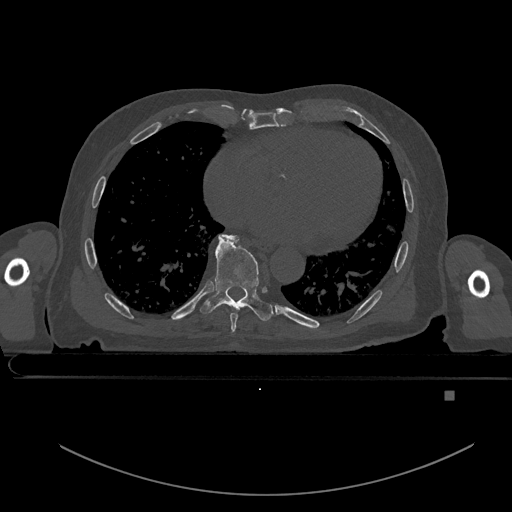
CT including the spine, one axial slice. Position 214 of 969 along the scan axis. Bone window (W 1800 / L 400 HU). 512 × 512 image matrix, field of view 456 × 456 mm. Male patient, age 82 years. Case-level facts recorded for this patient, not image findings: primary cancer: prostate; vertebrae with lytic lesions (as recorded): T11, T9, T8, T2.
Structures marked on this image (semi-automatically segmented with operator editing):
- T7 vertebra: box from (x=226, y=235) to (x=238, y=332) px
- T8 vertebra: (x=200, y=234)–(x=274, y=321)